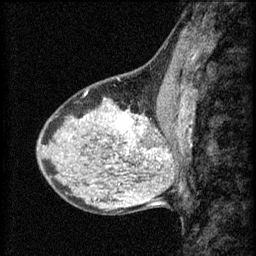
Breast MRI (dynamic contrast-enhanced), one sagittal slice; 3 images stored at this slice position (order not interpretable as contrast timing); 1.5 T; TE 4.2 ms, TR 8.2 ms; 256 × 256 image matrix, field of view 180 × 180 mm. Female patient, age 40 years.
Annotated regions visible in this slice (semi-automatically segmented with operator editing):
- analysis volume of interest (the breast-tissue region the enhancement analysis was run in; not a lesion): bounding box (x1, y1, x2, y2) in pixels: (108, 108, 167, 159)
- tumour enhancement mask (voxels above the 70 % enhancement threshold inside the analysis volume of interest): (116, 114, 167, 159)